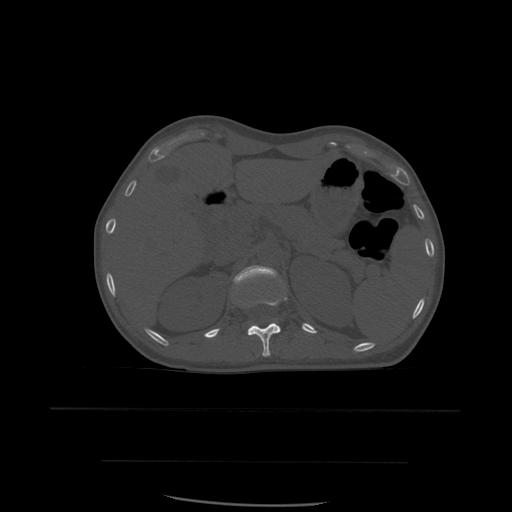
CT including the spine, one axial slice. Position 266 of 574 along the scan axis. Bone window (W 1800 / L 400 HU). 1.25 mm slice thickness. 512 × 512 image matrix, field of view 392 × 392 mm. Patient age 48 years. From the clinical record (not read from this slice): primary cancer: lung; vertebrae with lytic lesions (as recorded): T11.
Outlined on this slice (semi-automatic segmentation, software-assisted and operator-edited):
- L1 vertebra: bounding box <234,266,278,287> (left, top, right, bottom; pixels)
- T12 vertebra: <247,295,288,357>